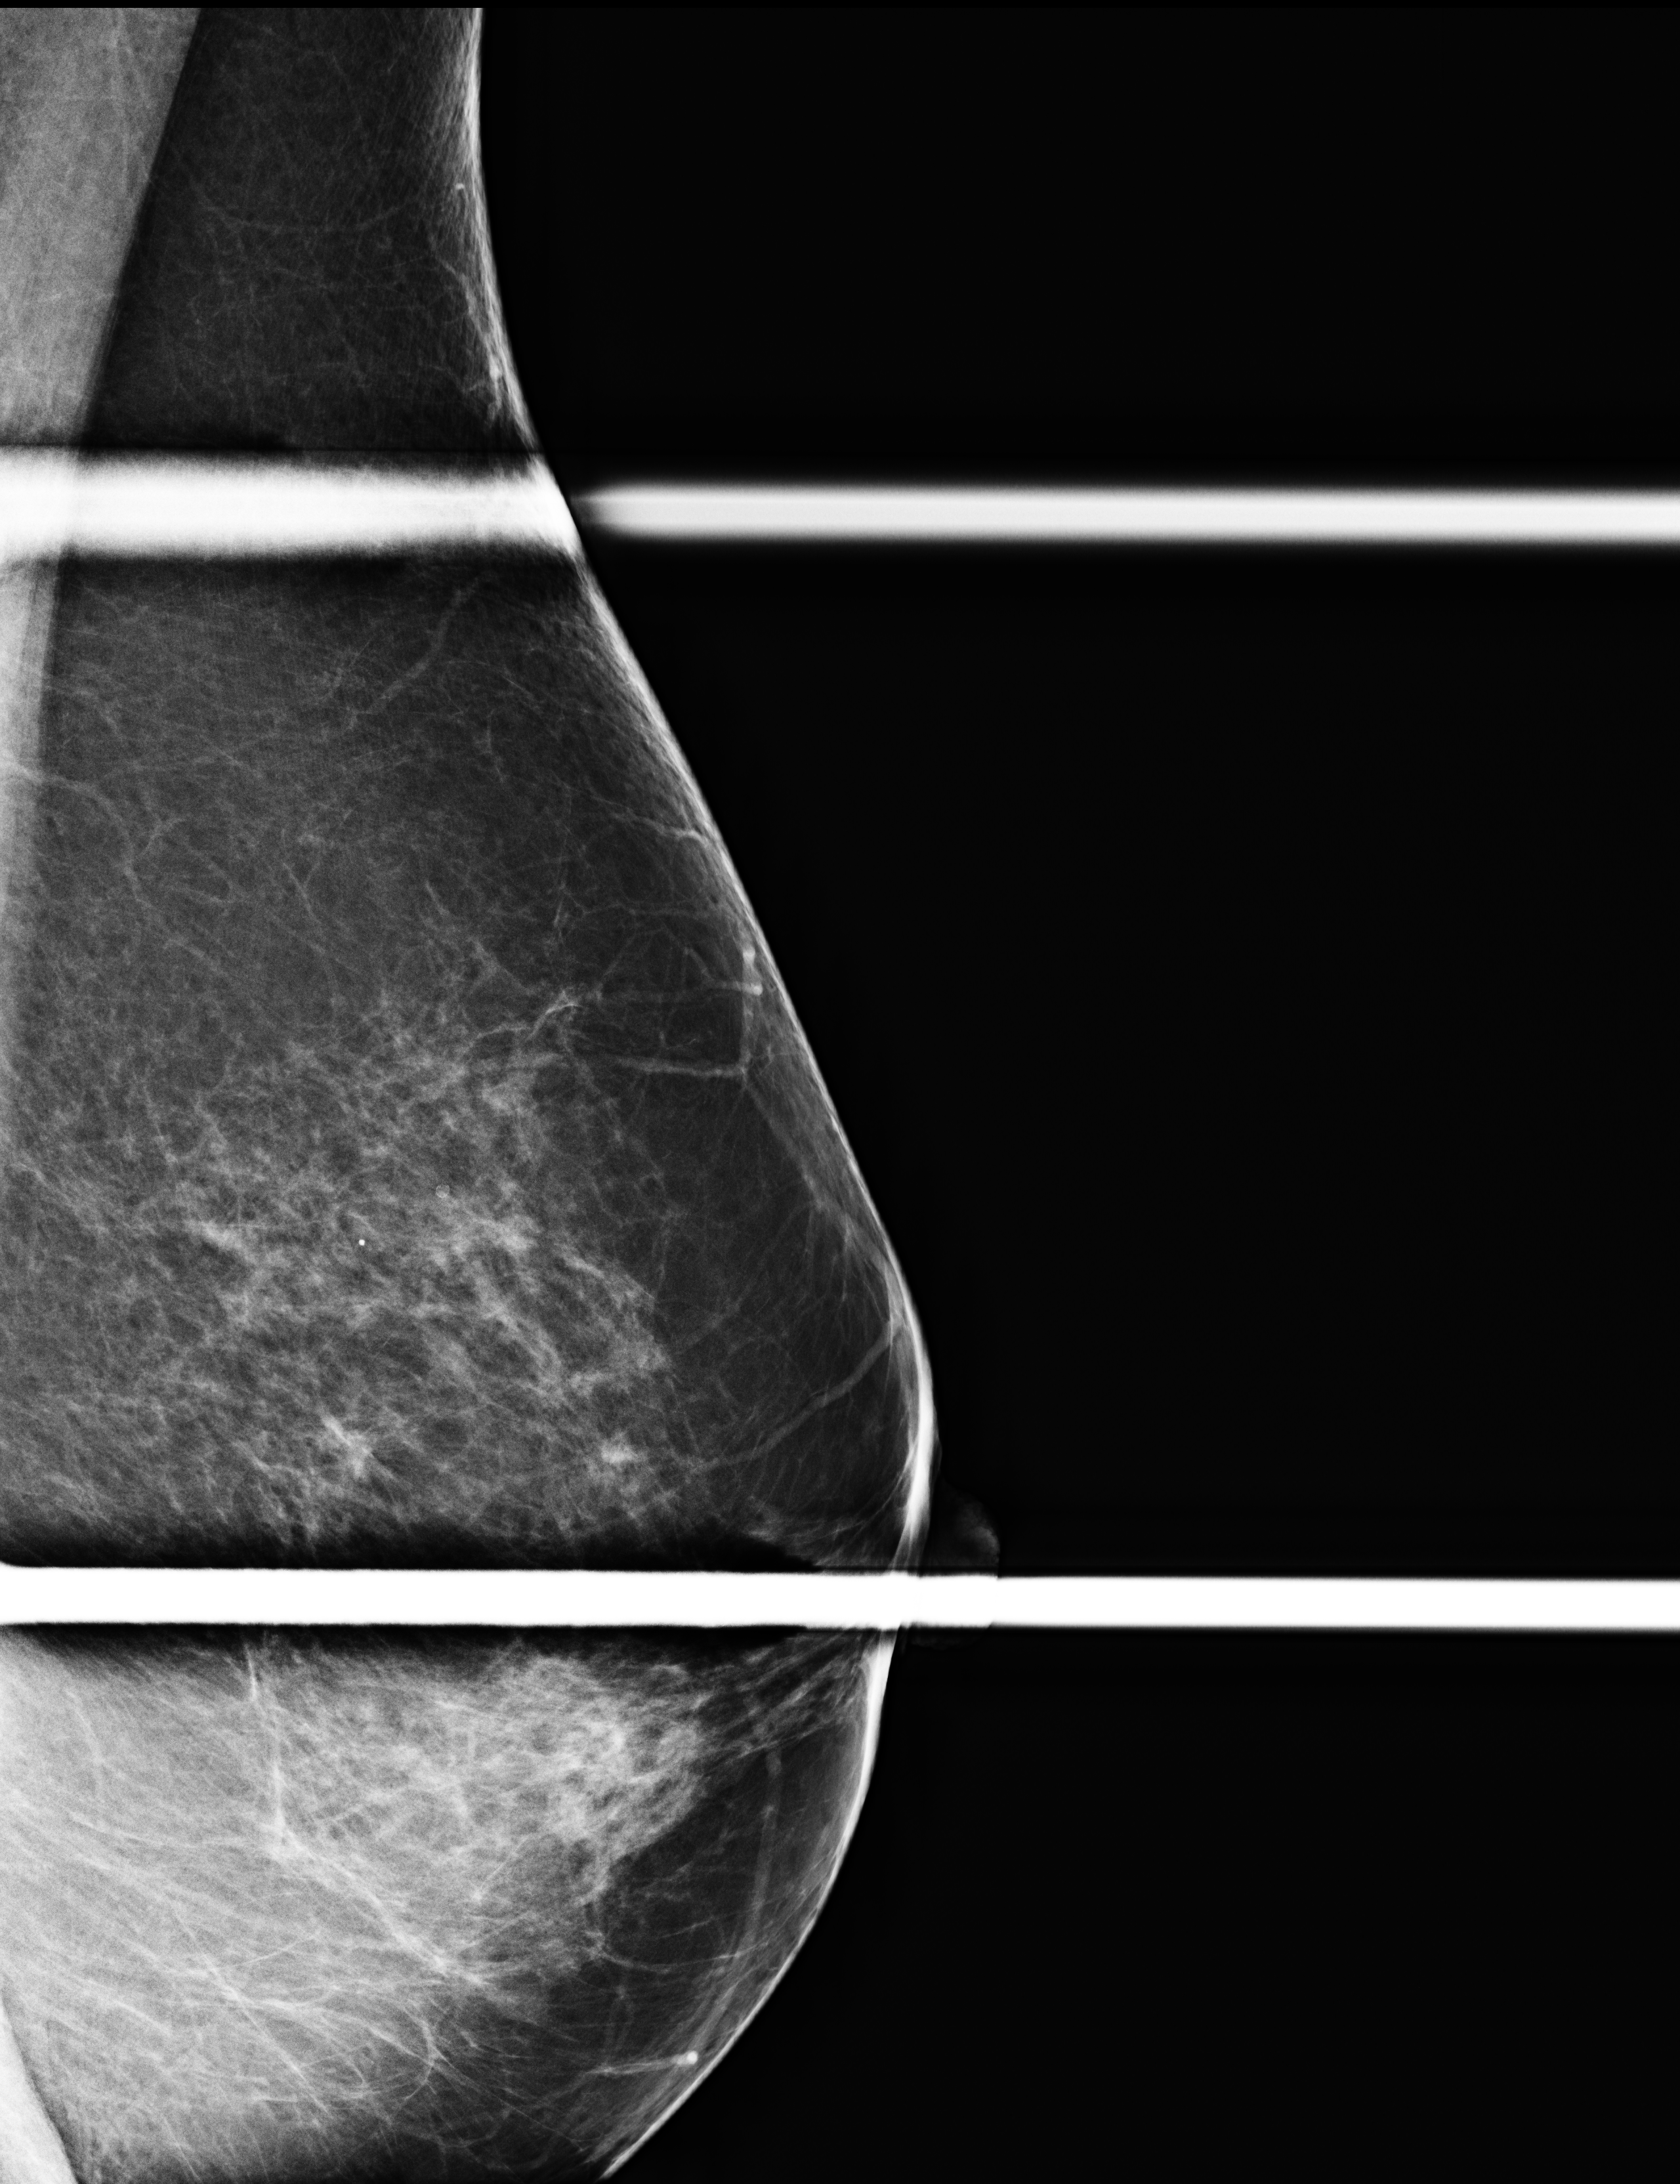
Full-field digital mammogram (FFDM), left breast, ML view (spot compression), additional work-up view, compressed breast thickness 67 mm. Female patient, age 74 years.
Breast density at the screening exam (both breasts): heterogeneously dense (BI-RADS density category c). Final BI-RADS assessment for this screening round (tomosynthesis exam, both breasts): category 4. Recall: recalled for additional imaging after this screen.